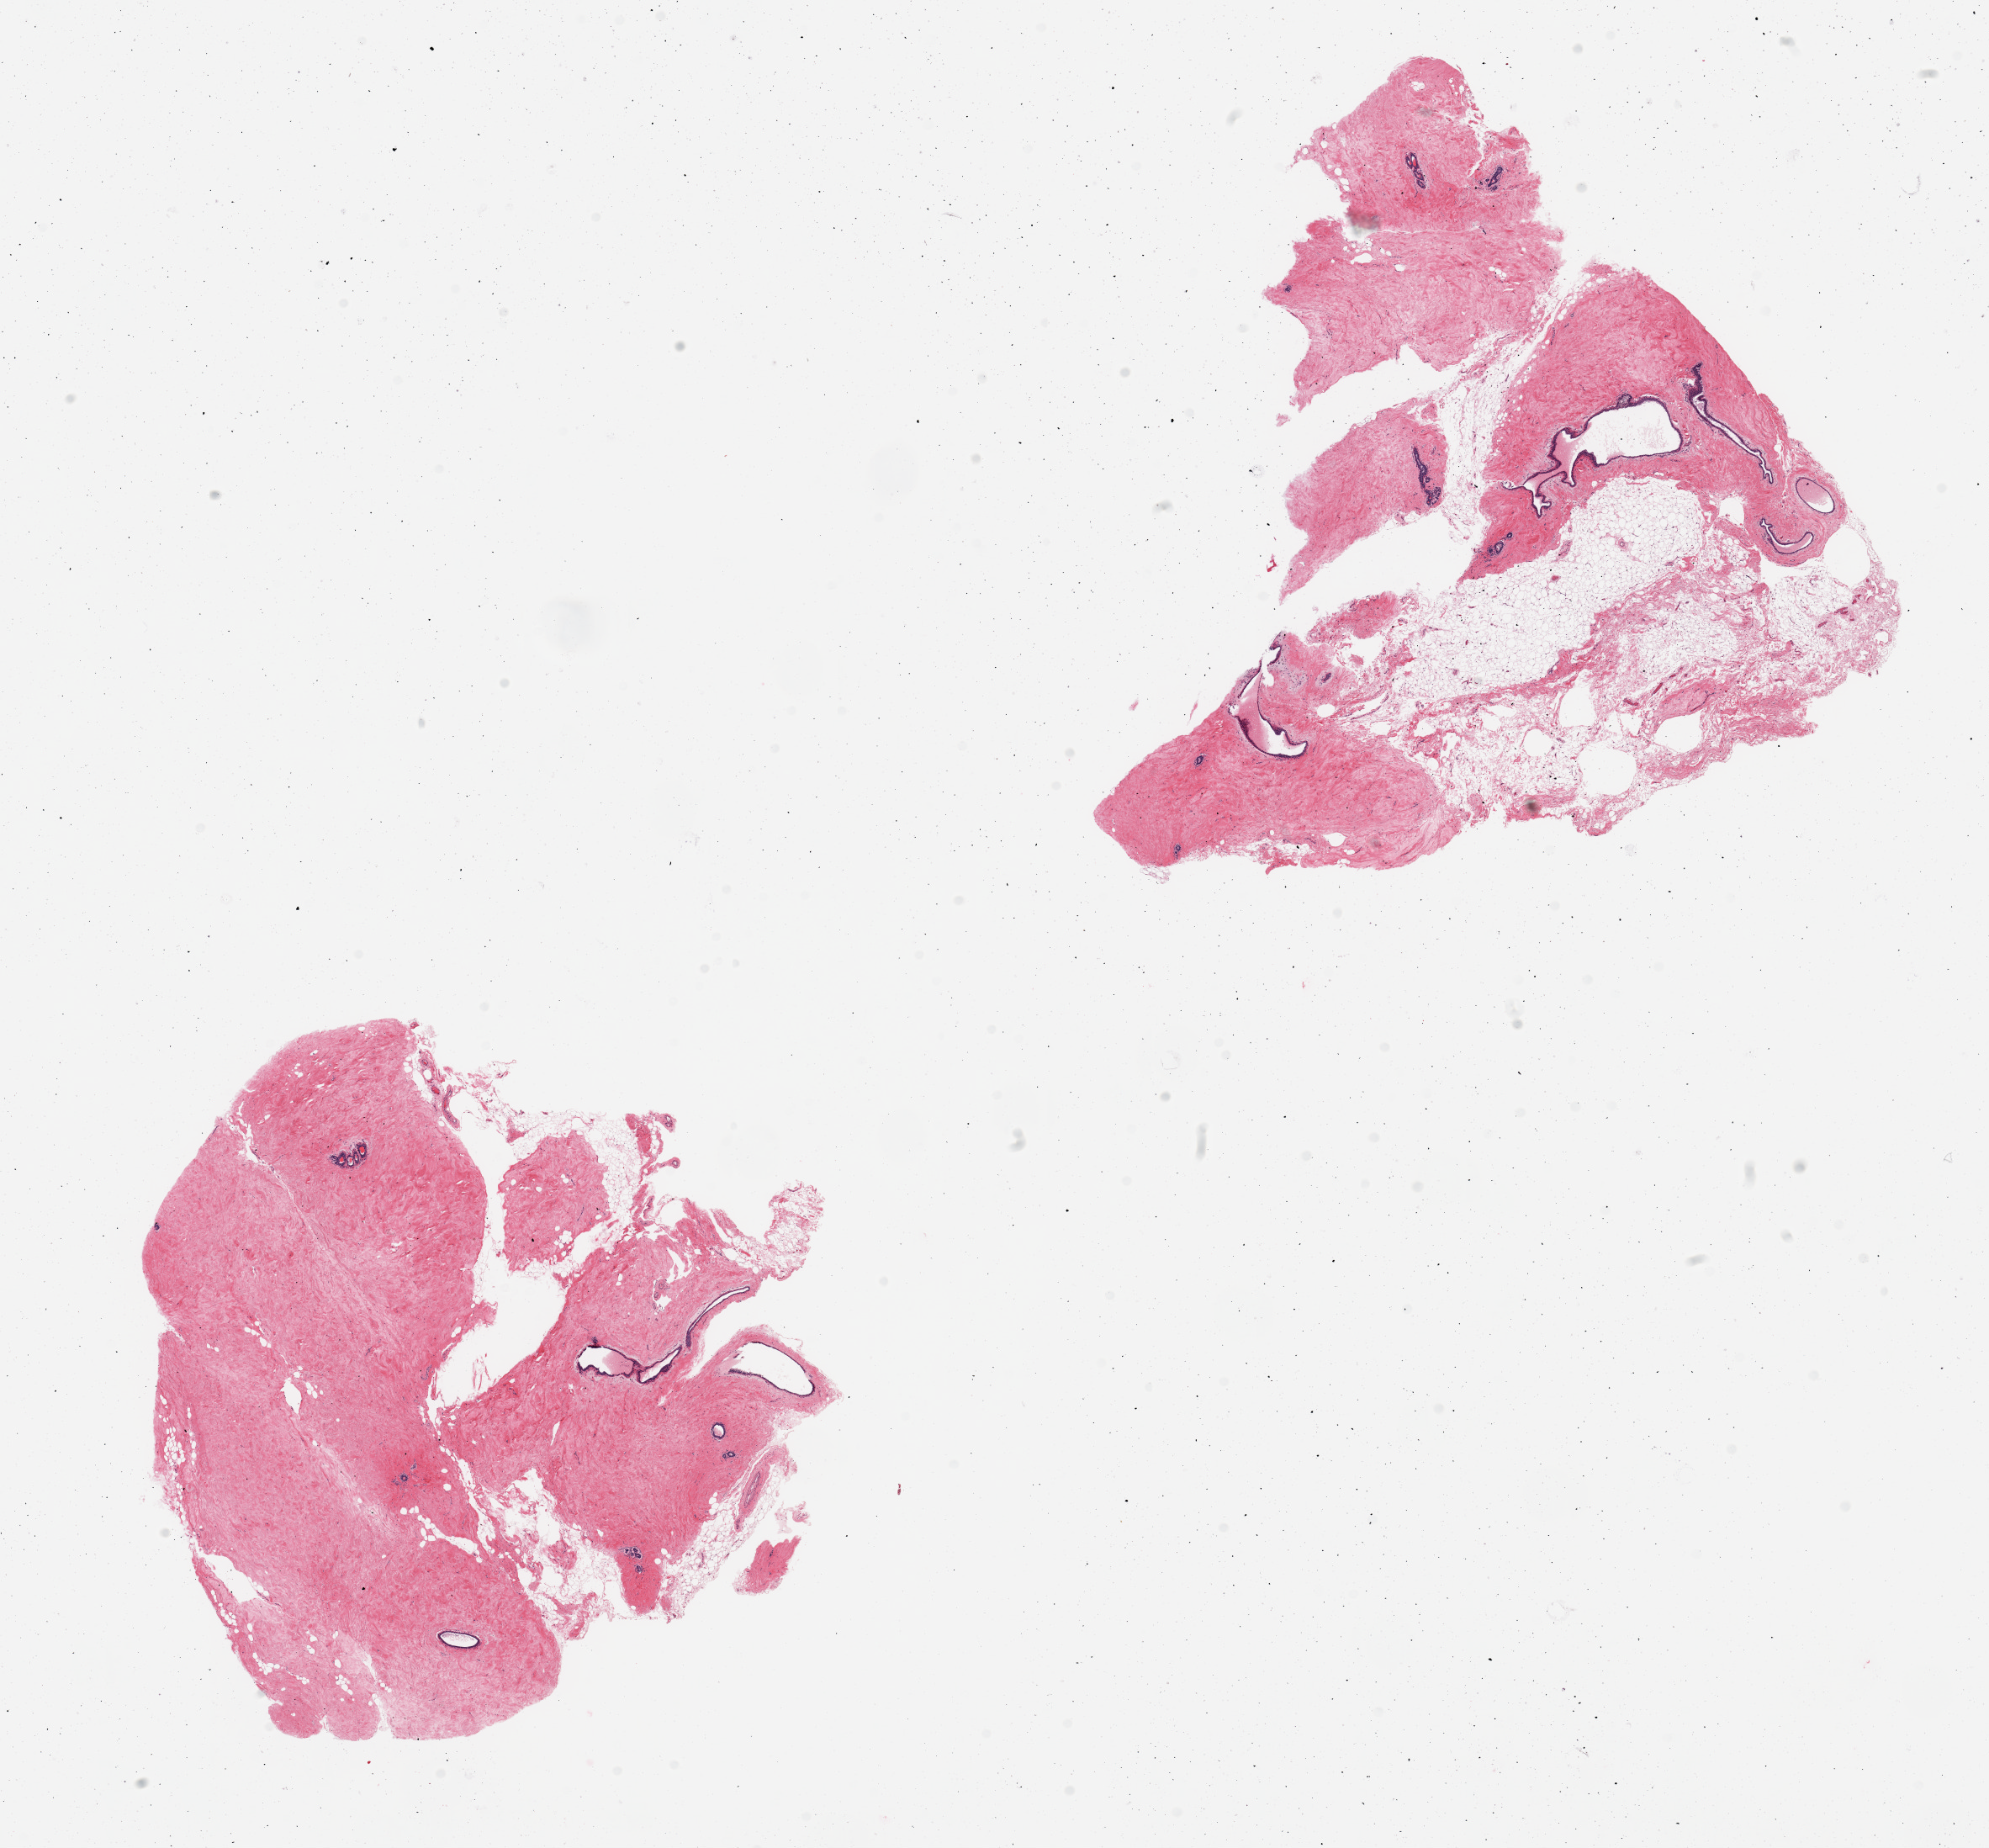
Digitized haematoxylin and eosin-stained section, whole scanned area (about 18.7 x 17.4 mm, from a 20x scan) shown as a low-resolution overview; PAXgene-fixed paraffin-embedded (PFPE) section; section of breast (target tissue); donor tissue sample. Donor sex: female.
Review note (as recorded): 2 pieces; atrophic with fibrocystic change; ducts, no lobules.